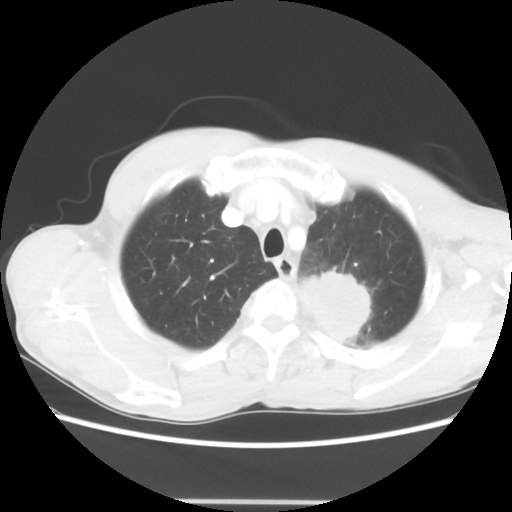
Chest CT, one axial slice. Slice 54 of 62 in the series (ordered by position). Reconstruction kernel STANDARD. 100 kVp. Lung window (W 1500 / L -600 HU). 512 × 512 image matrix, field of view 360 × 360 mm. Patient: male, 61 years. Case-level facts recorded for this patient, not image findings: clinical TNM (as recorded): T3 N1 M1.
Outlined on this slice (rectangle marked by the reading radiologist):
- lung tumour (recorded histology: adenocarcinoma): bounding box [x1, y1, x2, y2] px = [296, 262, 378, 347]